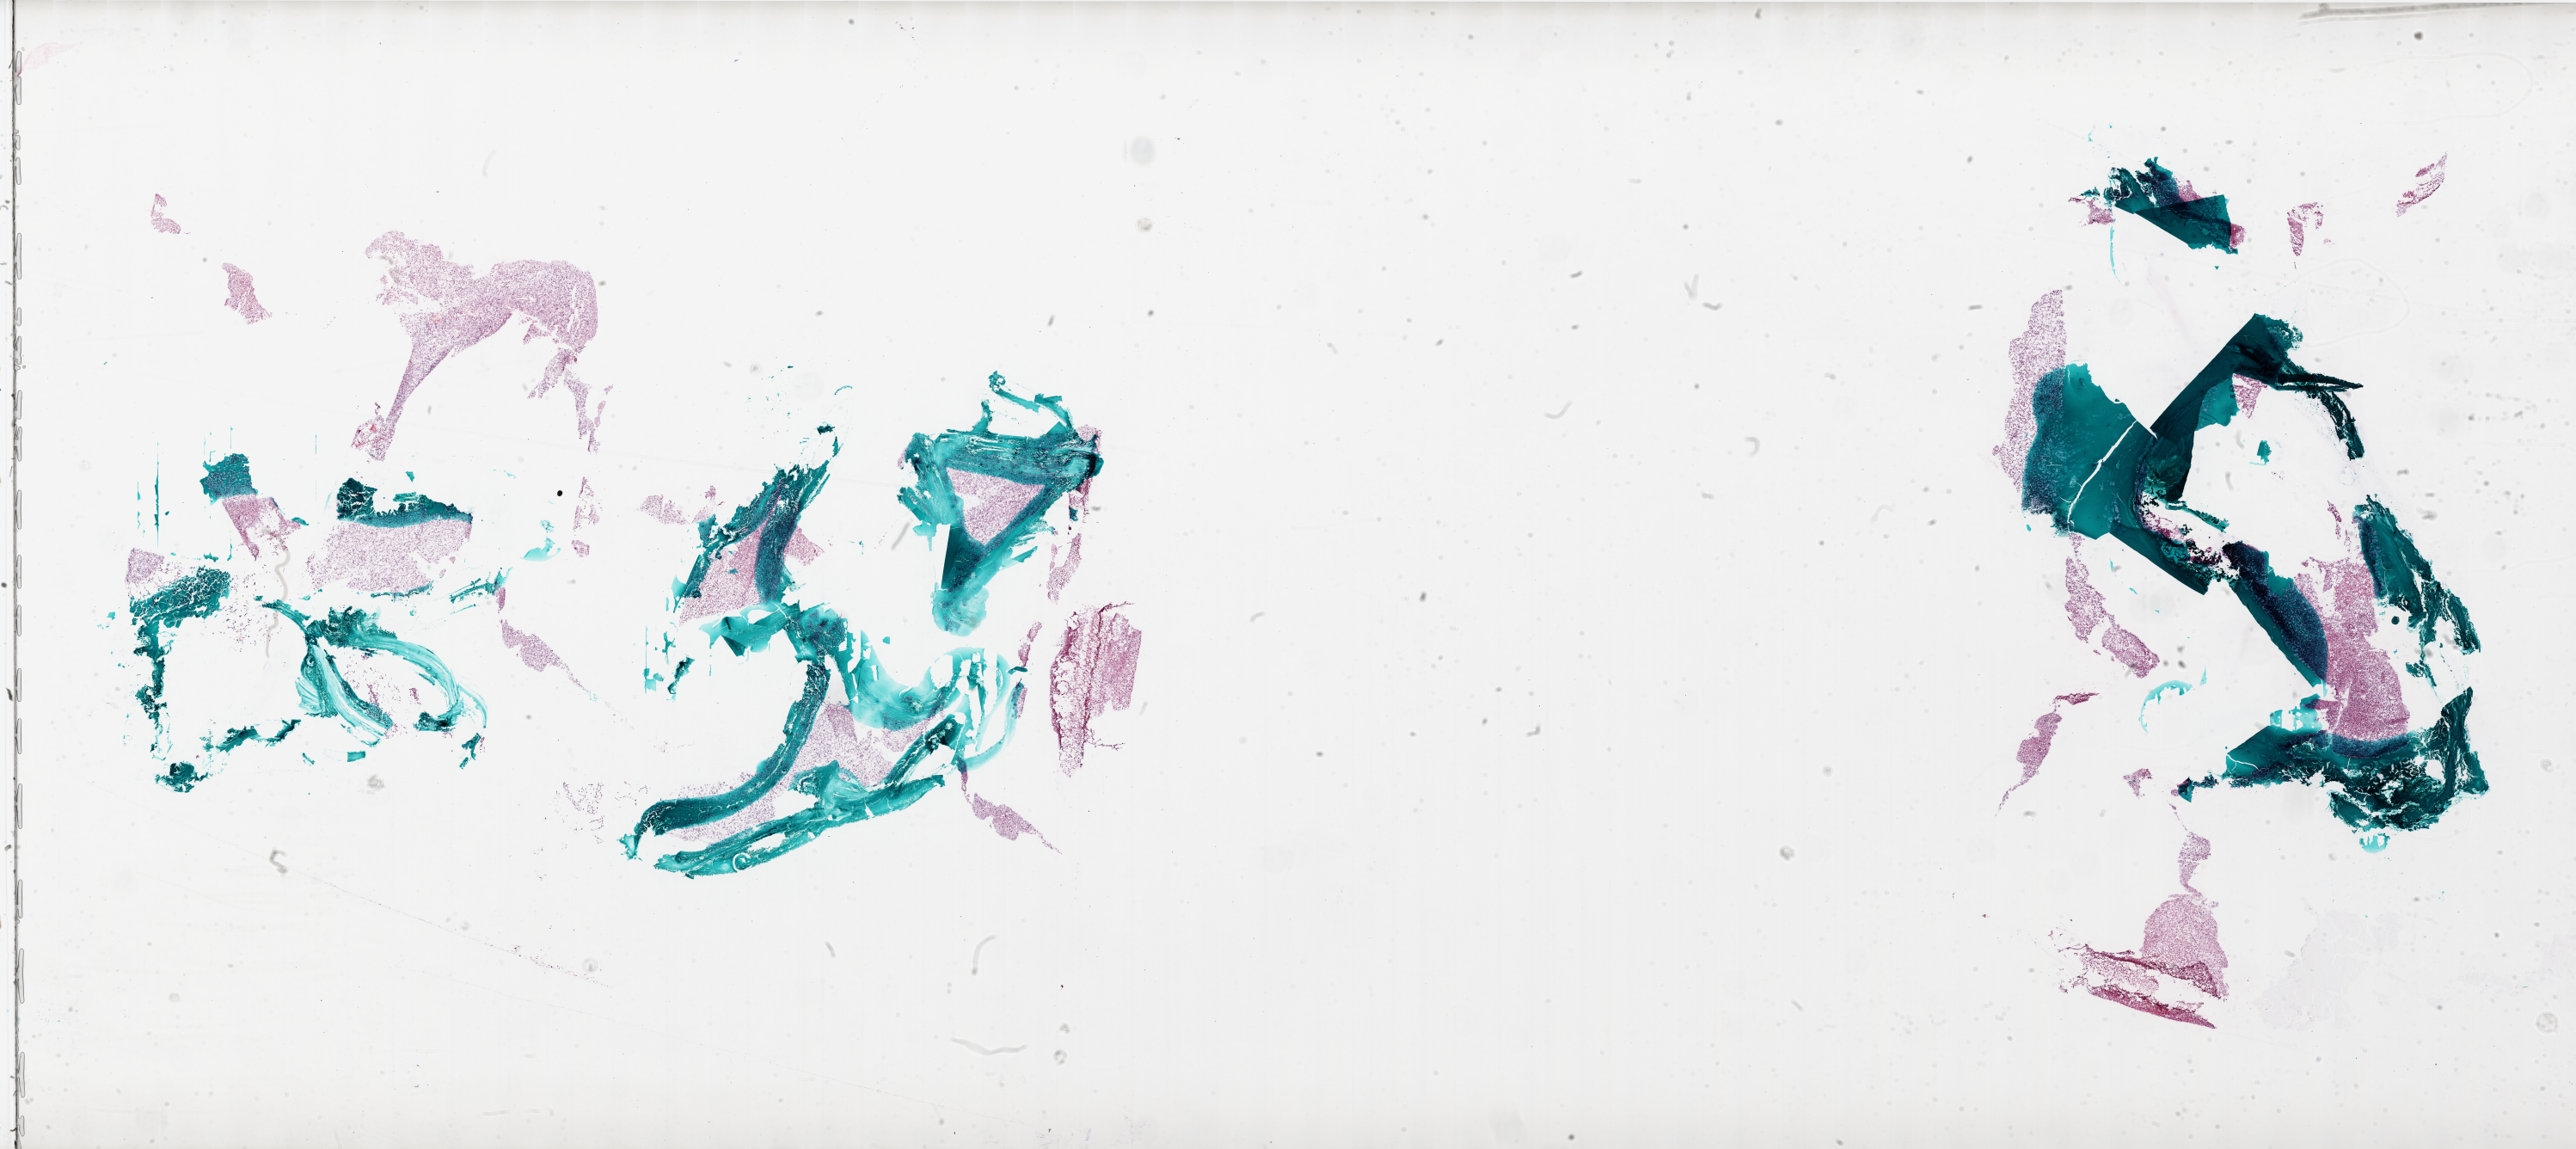
Whole-slide histology image, Hematoxylin and eosin (H&E) stained, low-resolution overview of the scanned area, about 48.0 x 21.4 mm; frozen section; brain, primary tumour sample. Patient: female, age at initial diagnosis 68 years. Pathologist review of this section (percent, as recorded): tumour cells 95%, tumour nuclei 100%.
Pathologic diagnosis: Glioblastoma.